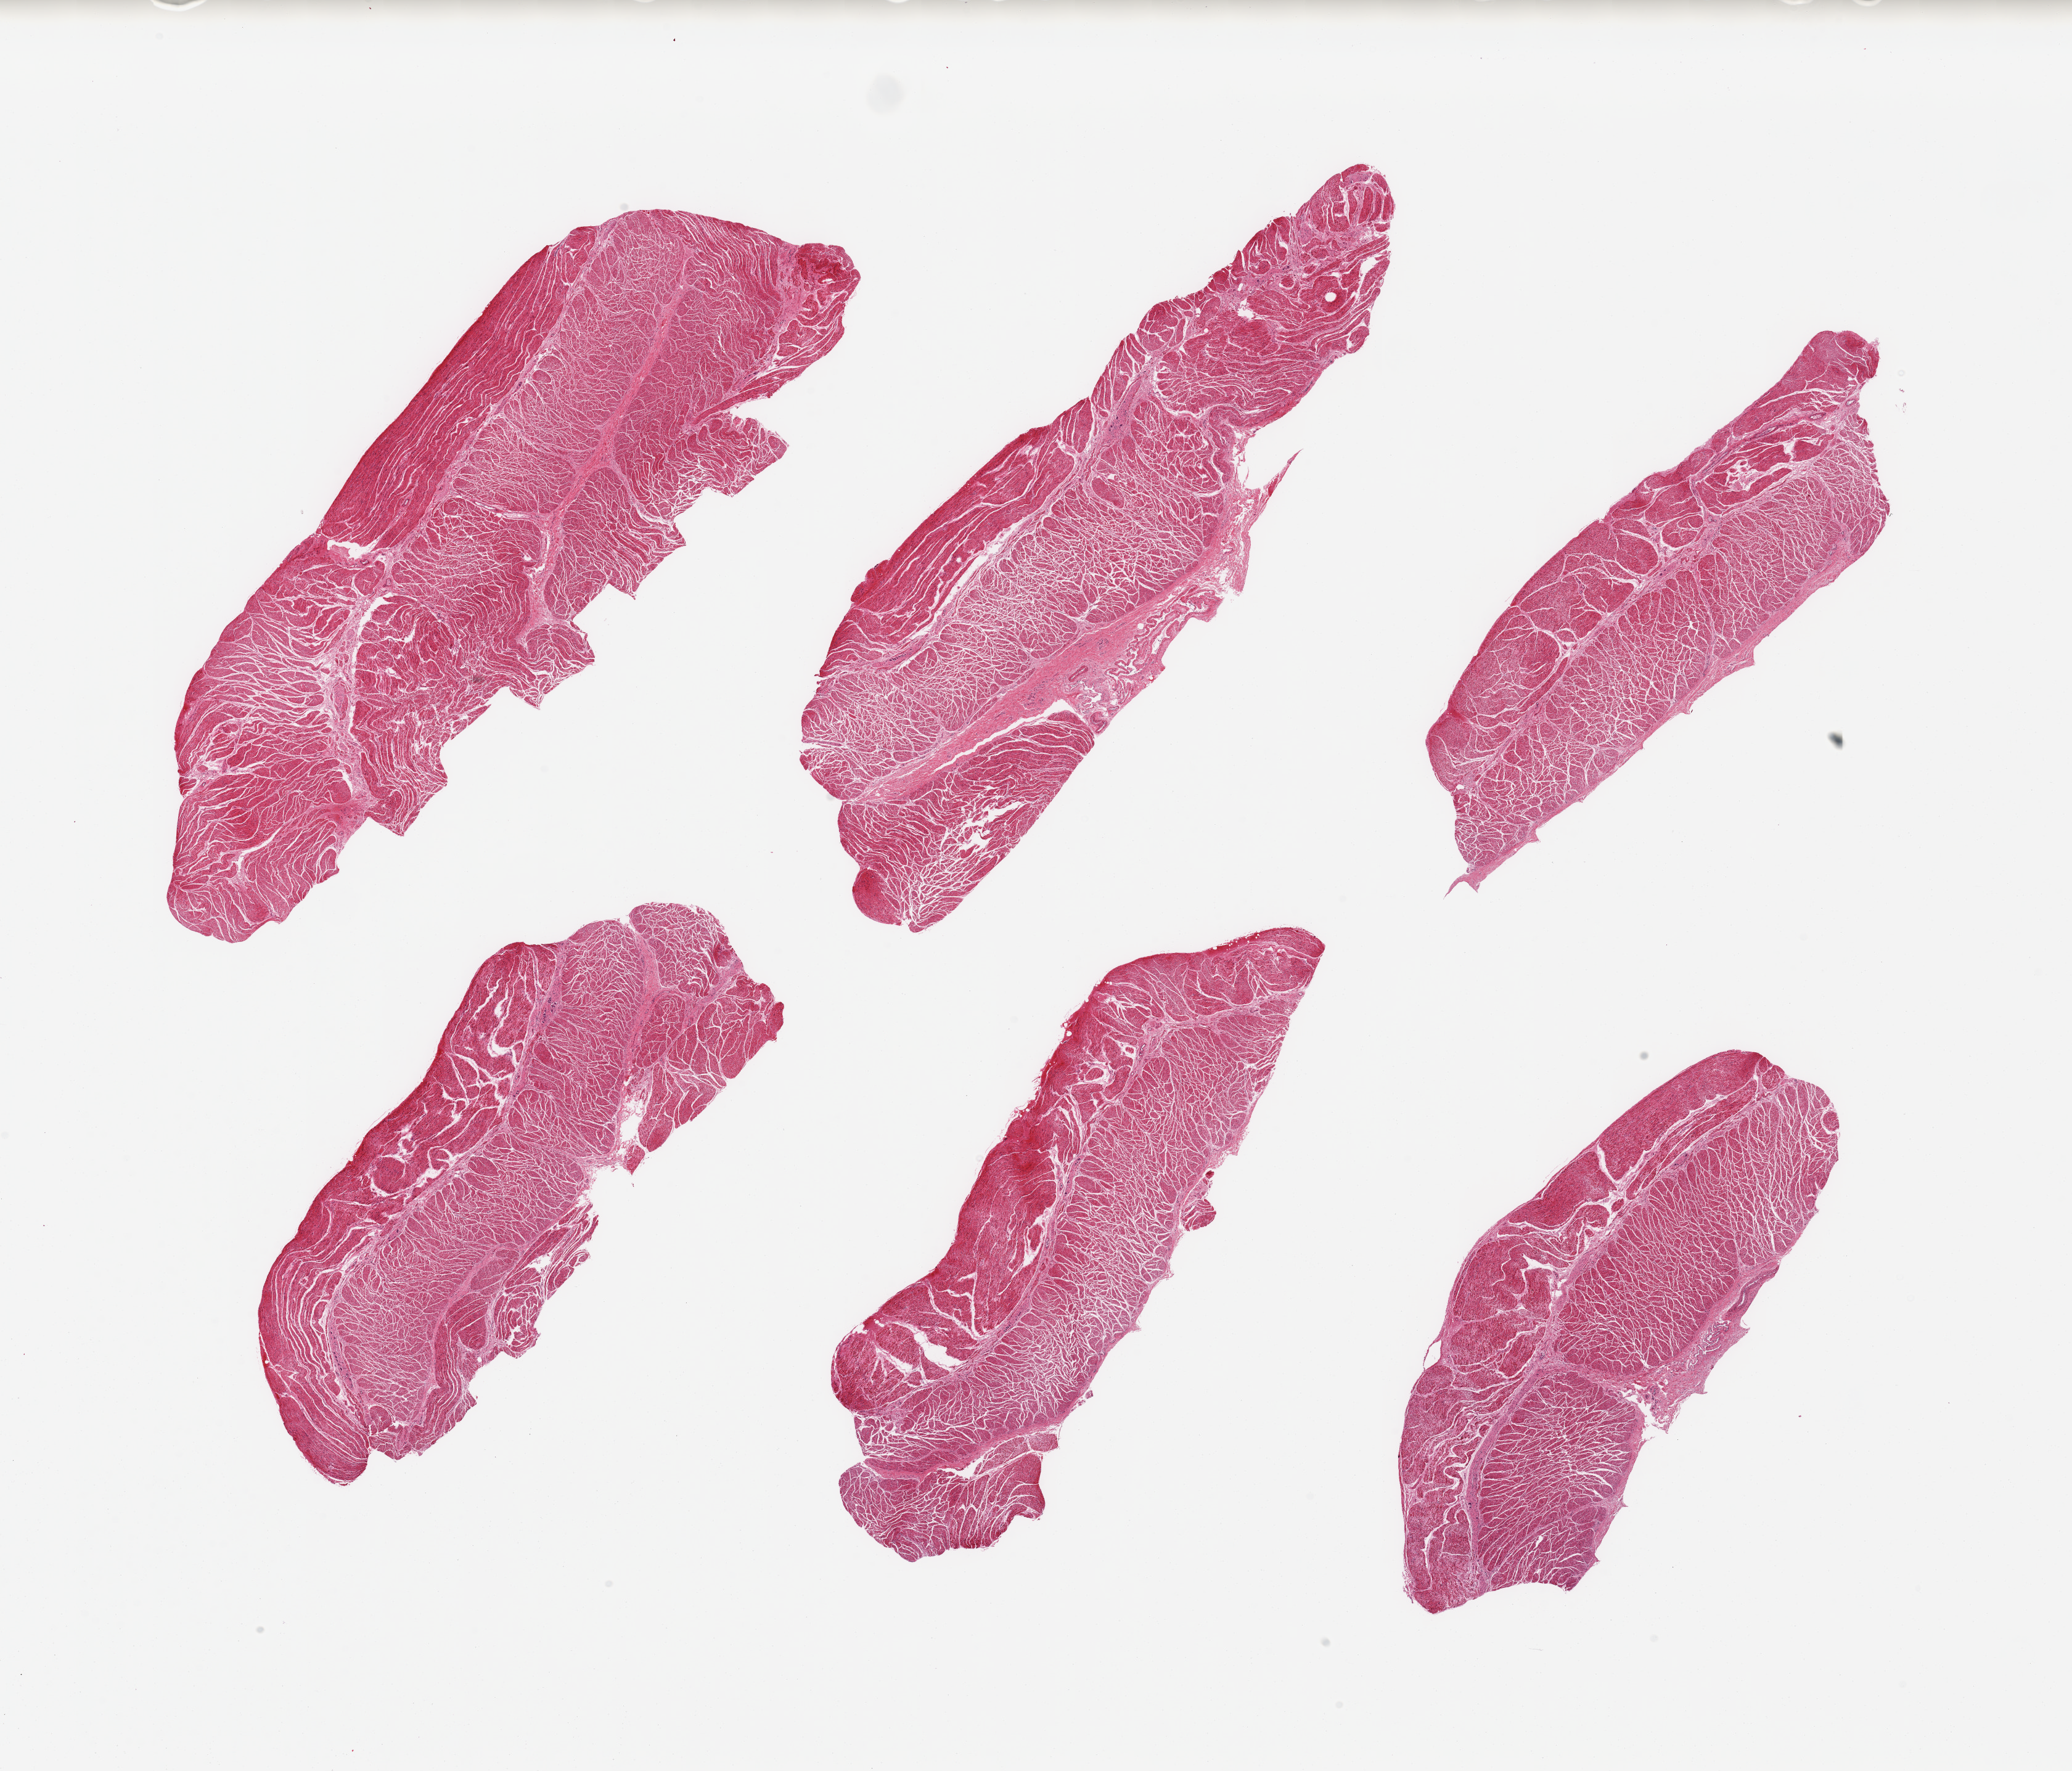
Digitized haematoxylin and eosin-stained section, whole scanned area (about 26.6 x 22.7 mm, from a 20x scan) shown as a low-resolution overview; PAXgene-fixed, paraffin-embedded tissue; target tissue: esophageal muscle; donor tissue sample. Female donor.
Review note (as recorded): 6 pieces; well dissected muscularis propria.